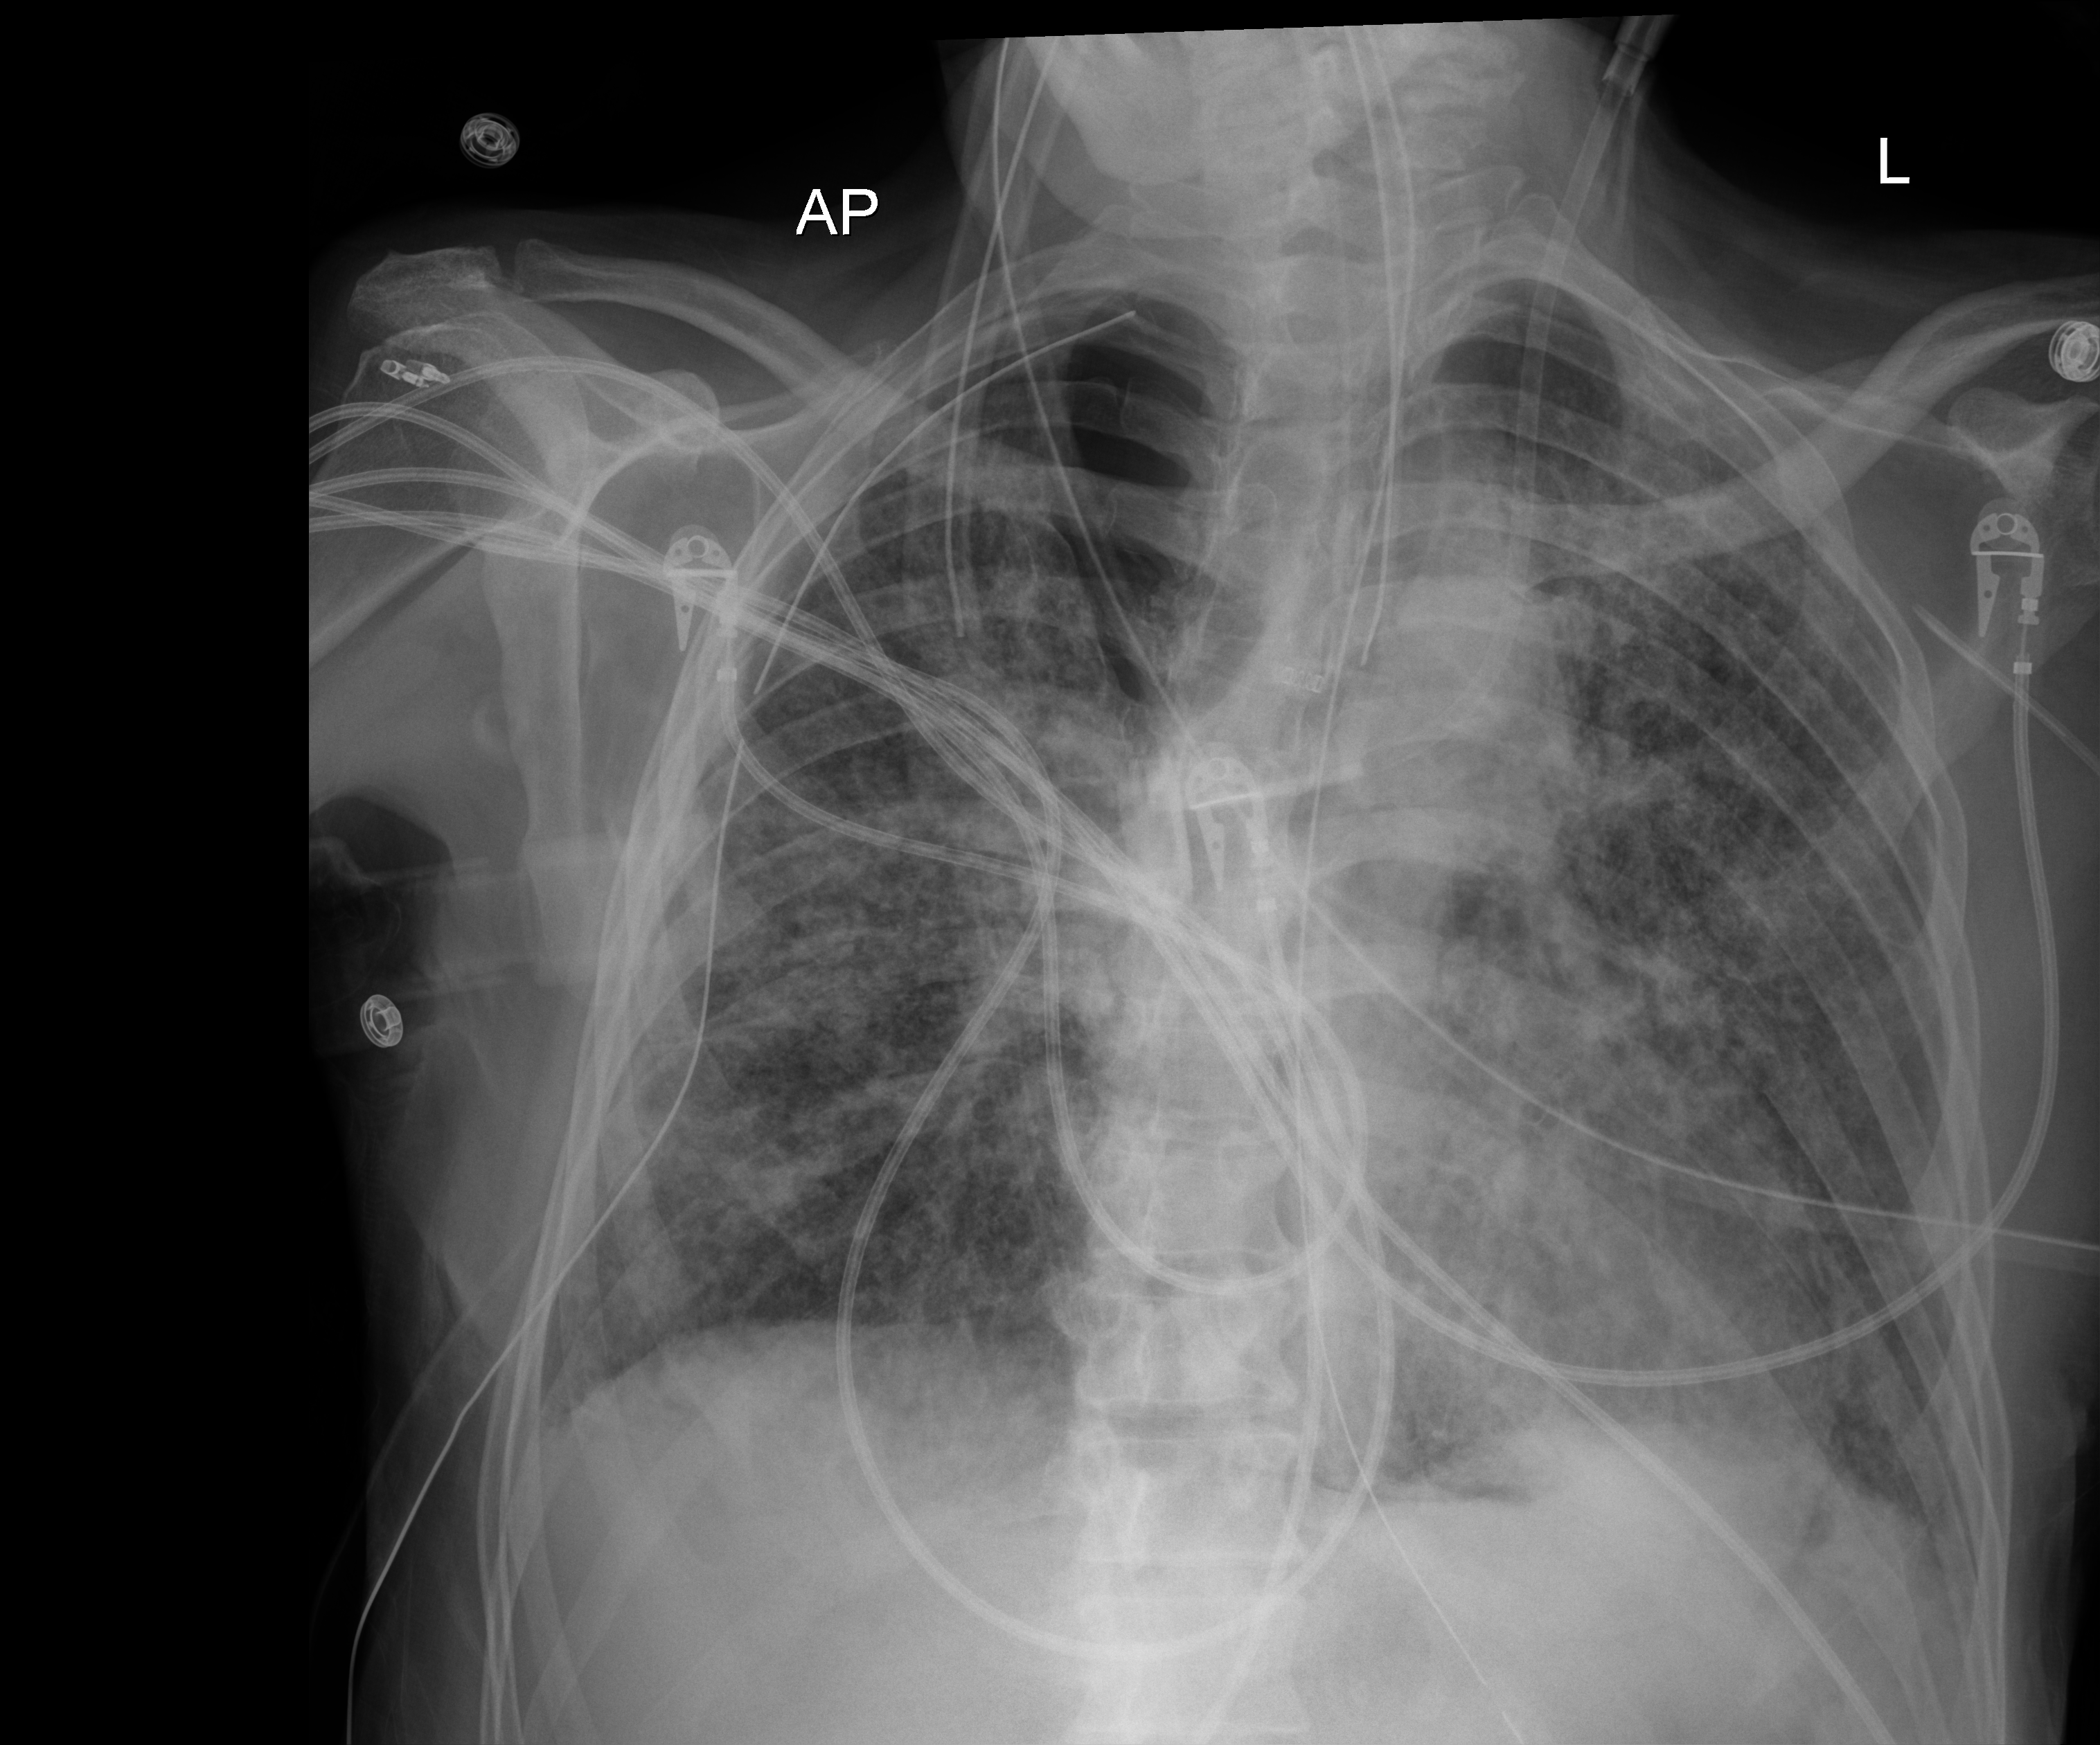
Bedside chest radiograph (digital radiography); anteroposterior (AP) projection. Male patient hospitalised with COVID-19, age 60–74 years.
From the hospital-stay record, not from the radiograph (when in the stay this image was taken is not recorded): admitted to intensive care during this hospital stay: yes.